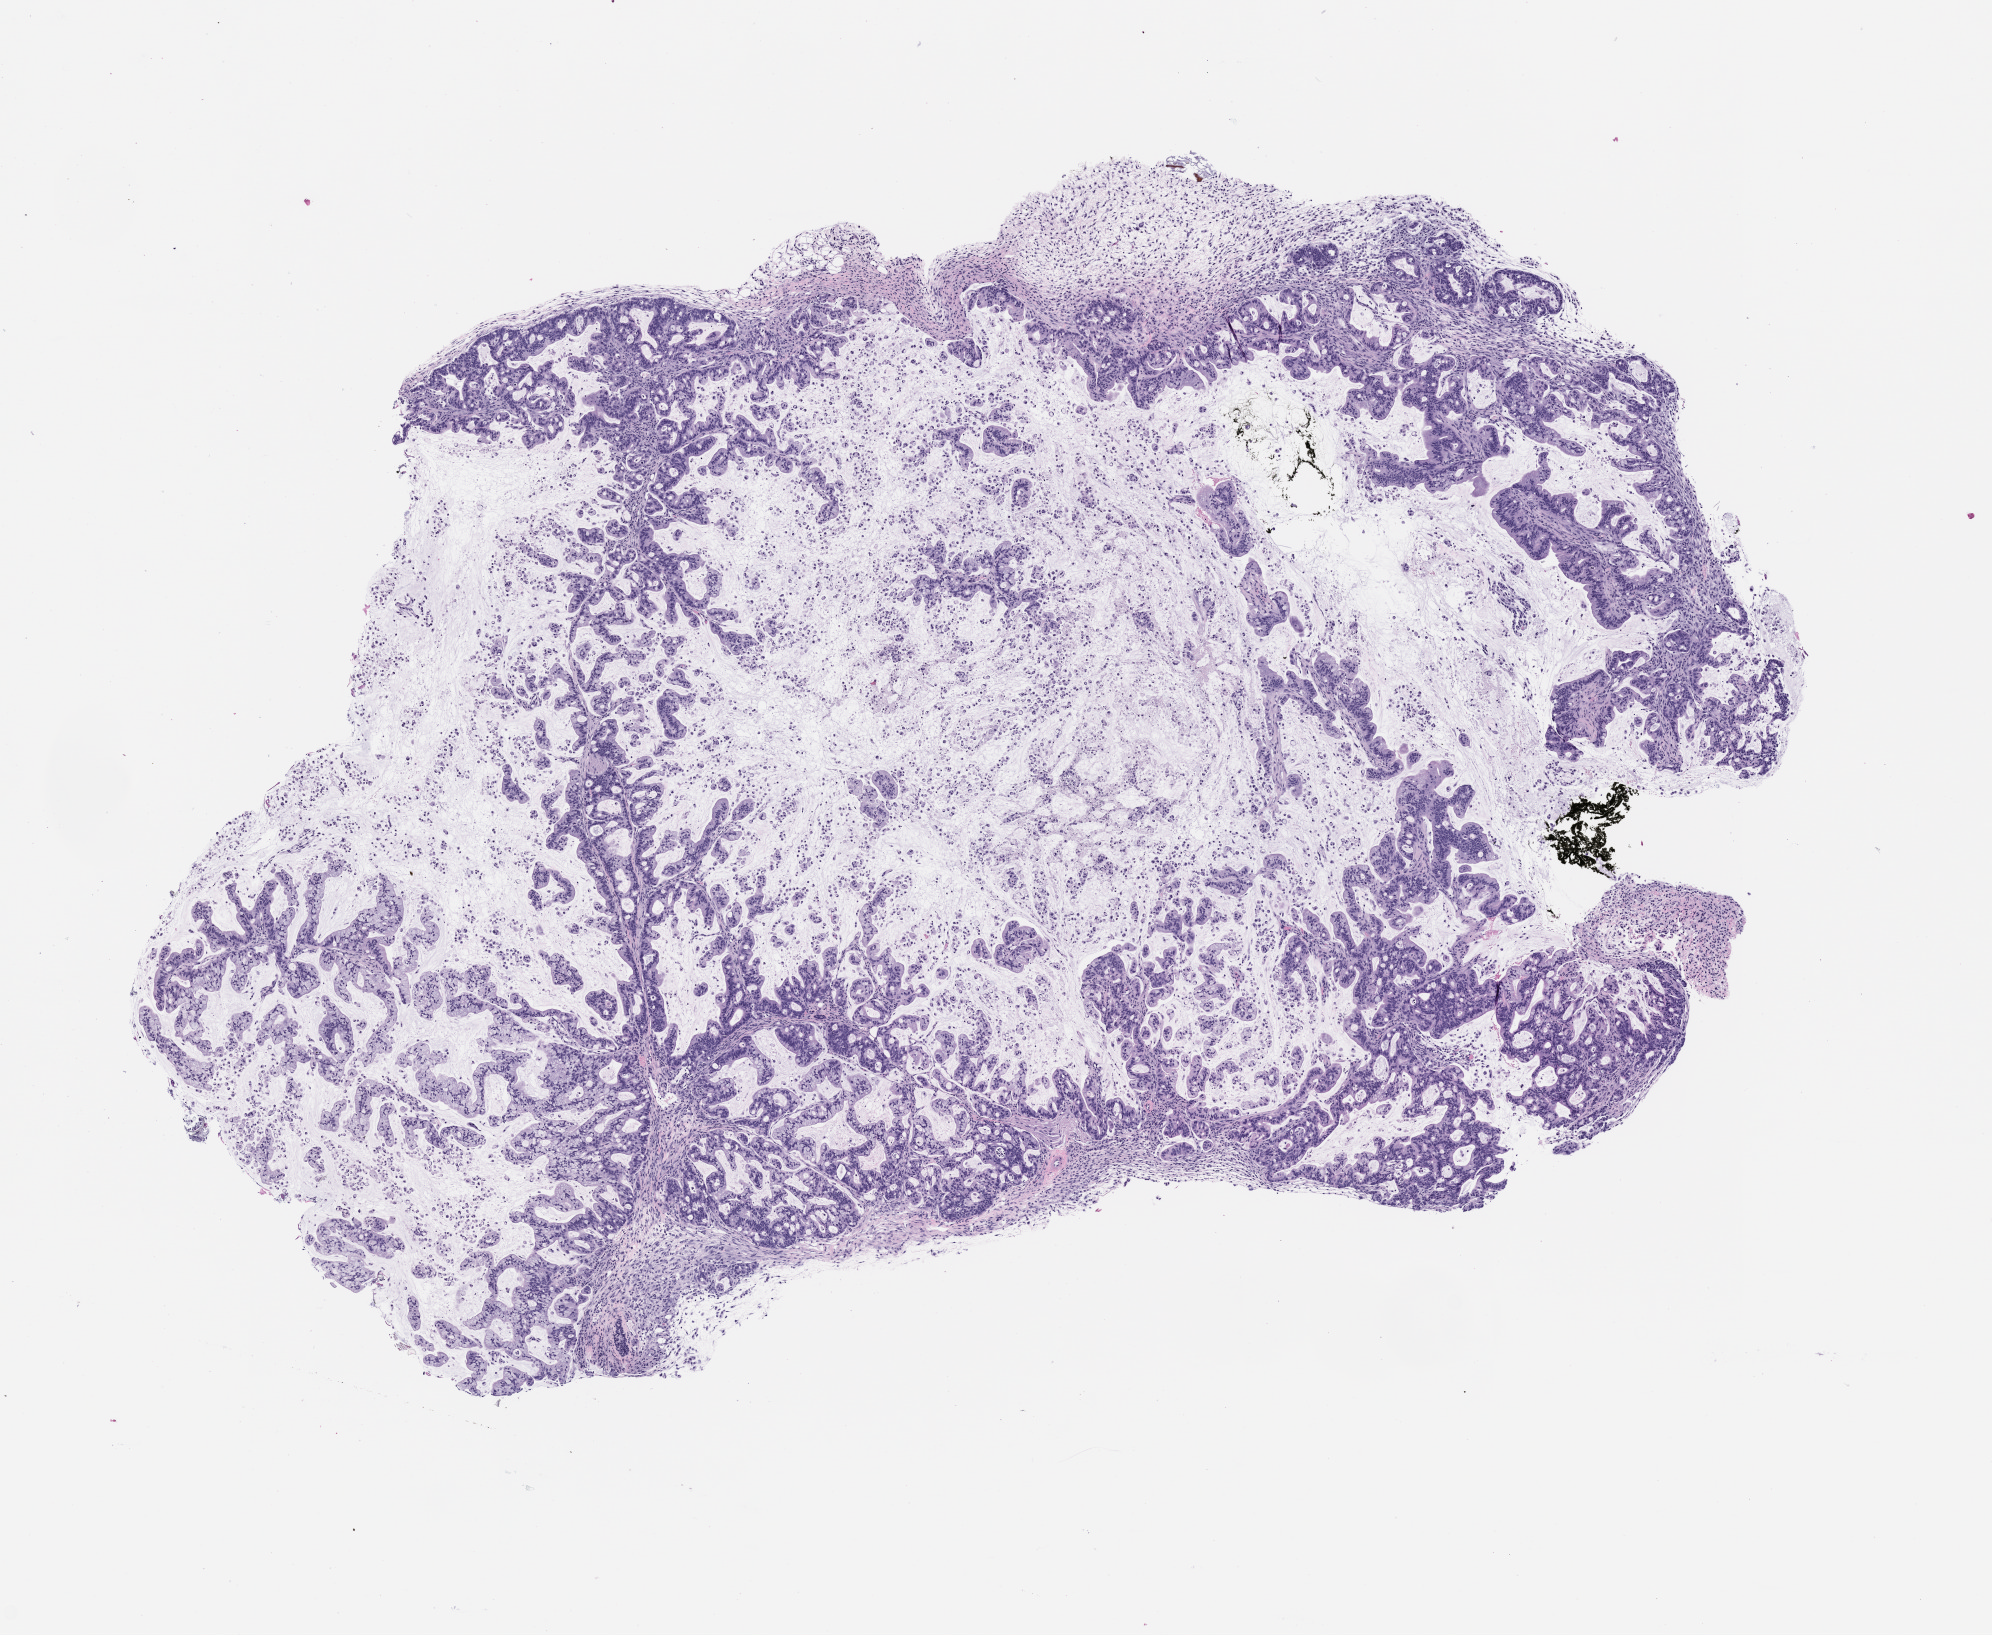
Whole-slide image, H&E: patient-derived xenograft (human tumor grown in a mouse), passage 1, low-resolution overview of the scanned area, about 8.0 x 6.6 mm; formalin-fixed, paraffin-embedded (FFPE) tissue; originating tumor site category: colon.
- originating patient diagnosis: Colon Adenocarcinoma